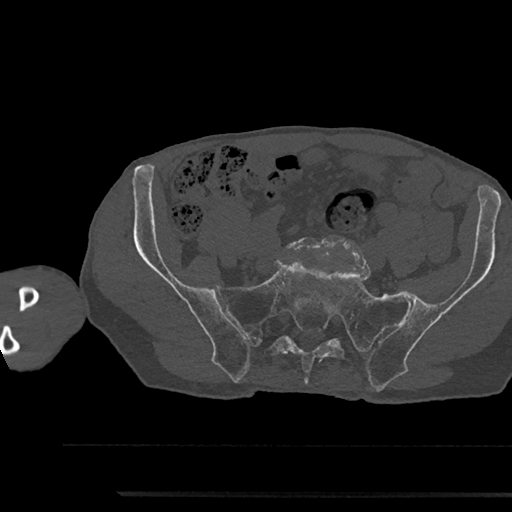
CT including the spine, one axial slice. Position 284 of 797 along the scan axis. Bone window (W 1800 / L 400 HU). 0.5 mm slice thickness. 512 × 512 image matrix. Male patient, age 79 years. From the clinical record (not read from this slice): primary cancer: prostate.
Structures marked on this image (semi-automatic segmentation, software-assisted and operator-edited):
- L5 vertebra: bounding box [x1, y1, x2, y2] px = [287, 237, 352, 252]